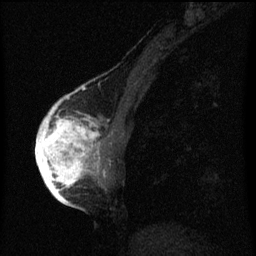
Breast MRI (dynamic contrast-enhanced), one sagittal slice; slice 25 of 60 in the series (ordered by position); dynamic contrast-enhanced series, image 2 of 3 at this slice position (ordered by acquisition); 1.5 T; TE 4.2 ms, TR 8 ms; 2 mm slice thickness; 256 × 256 image matrix, field of view 180 × 180 mm. Female patient, age 56 years.
Outlined on this slice (semi-automatic segmentation, software-assisted and operator-edited):
- analysis volume of interest (the breast-tissue region the enhancement analysis was run in; not a lesion): bounding box <42,110,105,193> (left, top, right, bottom; pixels)
- tumour enhancement mask (voxels above the 70 % enhancement threshold inside the analysis volume of interest): <42,110,101,193>